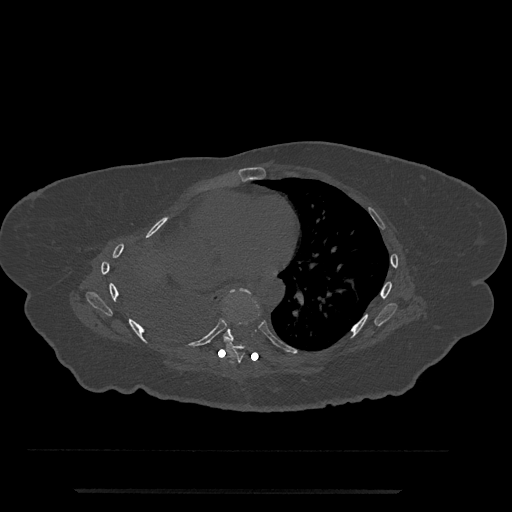
CT including the spine, one axial slice. Position 422 of 797 along the scan axis. 120 kVp. Bone window (W 1800 / L 400 HU). 0.5 mm slice thickness. 512 × 512 image matrix. Female patient, age 51 years. Case-level facts recorded for this patient, not image findings: primary cancer: neuro; vertebrae with lytic lesions (as recorded): T8.
Outlined on this slice (semi-automatically segmented with operator editing):
- T7 vertebra: bounding box [x1, y1, x2, y2] px = [224, 314, 261, 363]
- T8 vertebra: [223, 289, 250, 341]